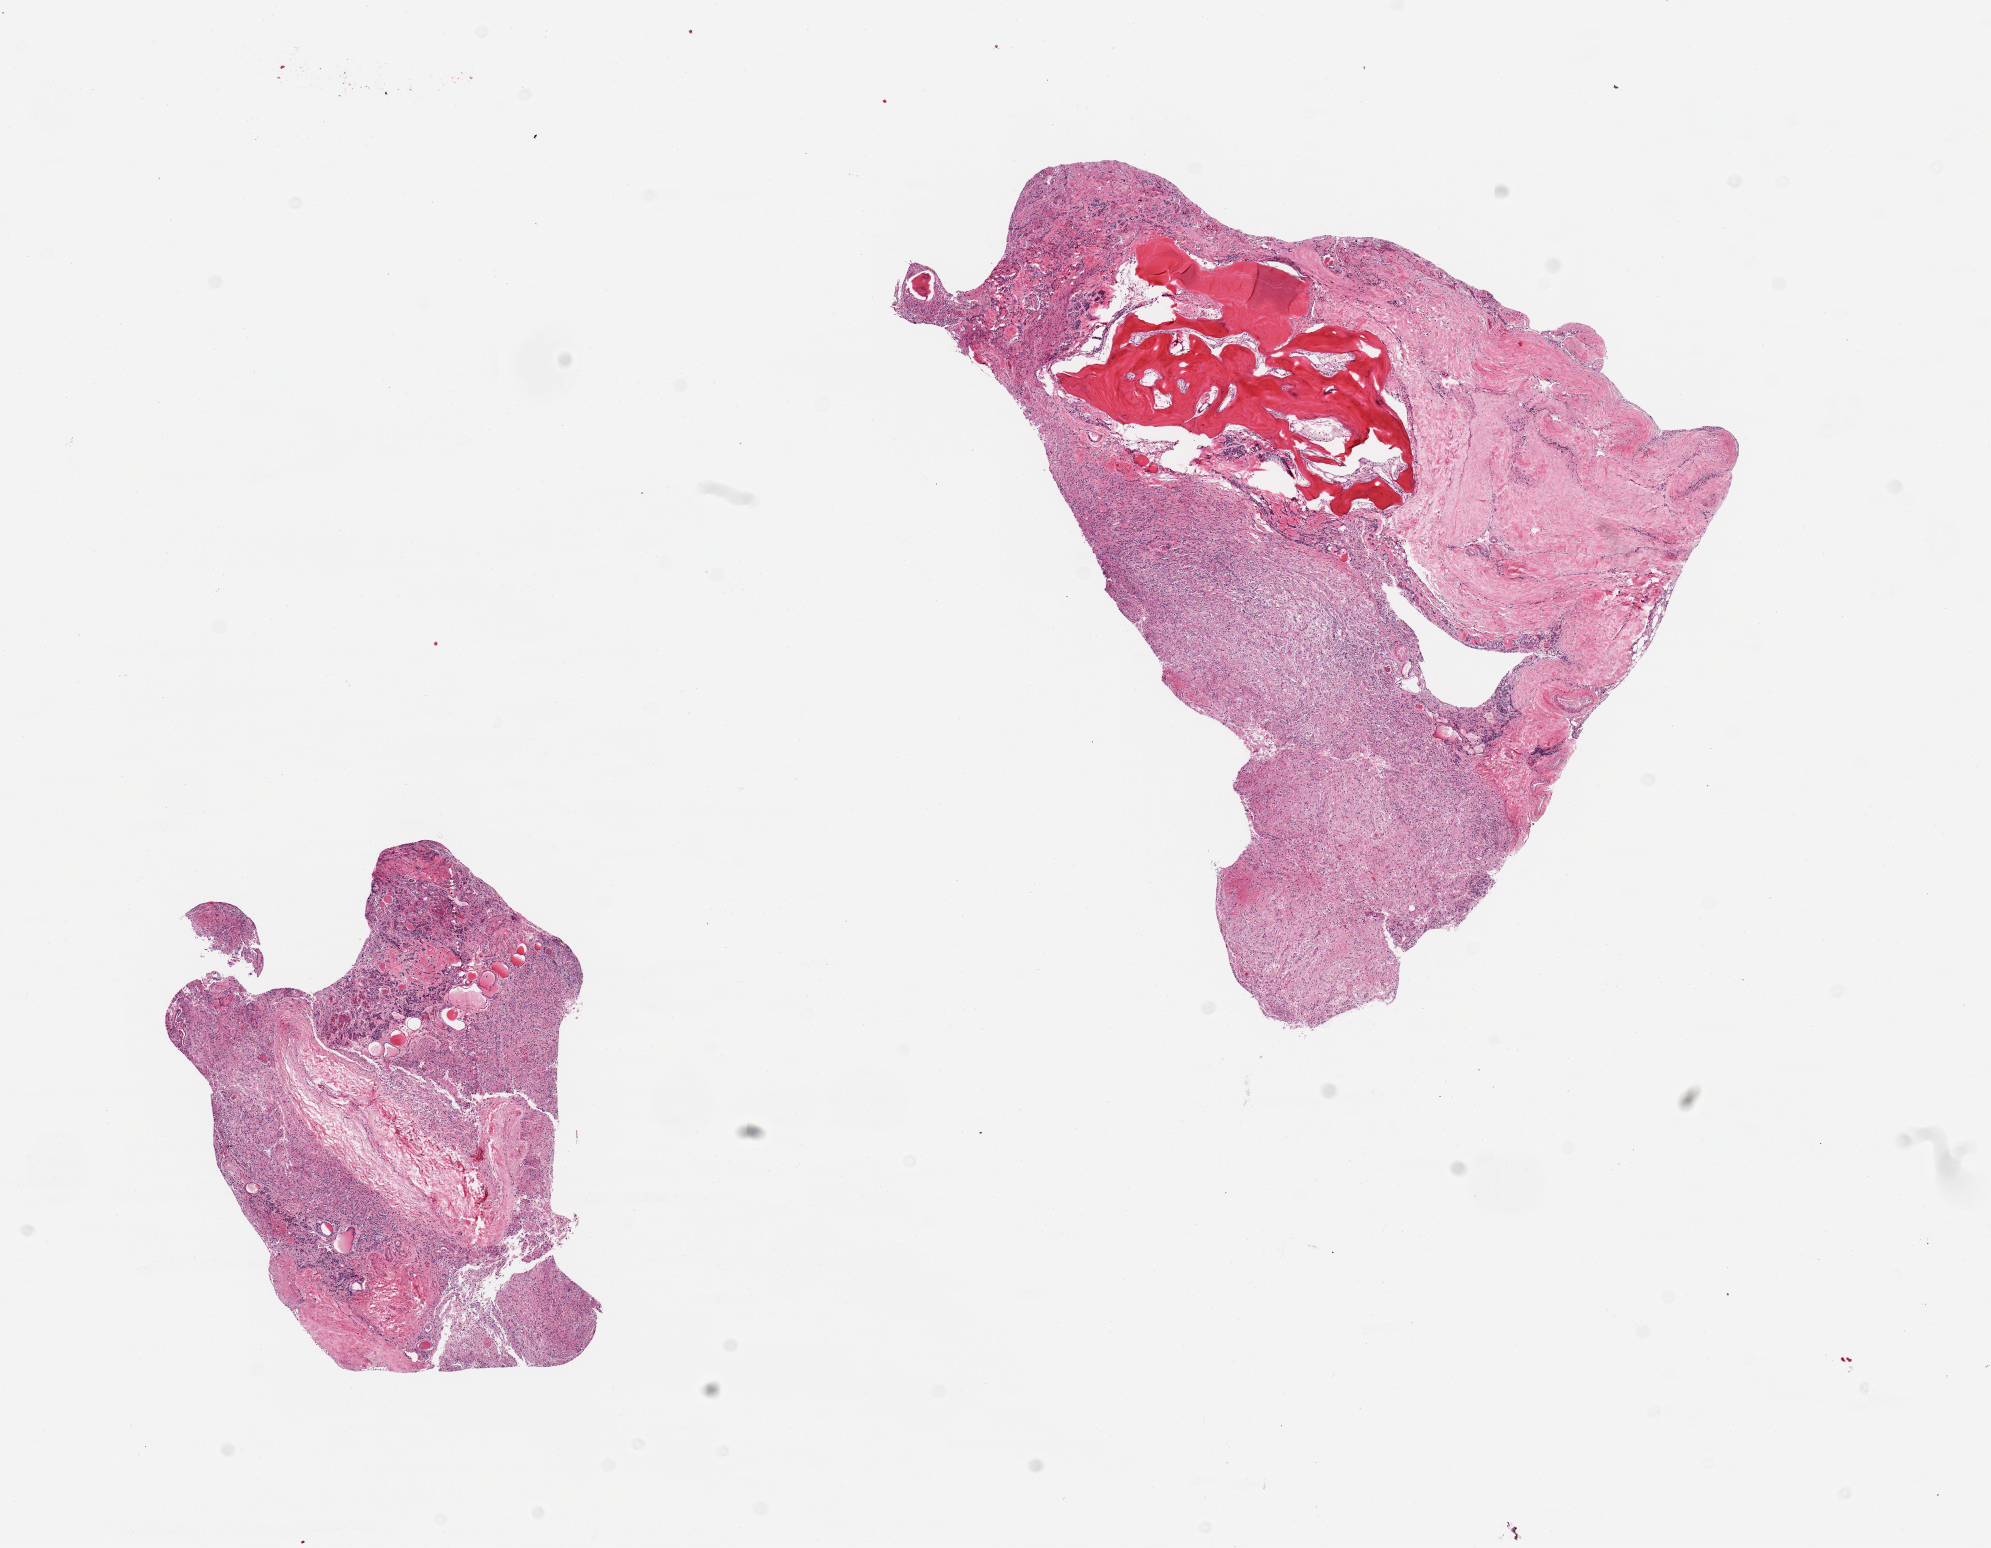
Whole-slide image, hematoxylin and eosin (H&E) stain, a low-resolution overview of the entire scanned area, about 15.8 x 12.2 mm (slide scanned at 20x). PAXgene-fixed paraffin-embedded (PFPE) section. Sampled site (target tissue): pituitary. Donor tissue sample. Donor: female.
* review note (as recorded): 2 pieces; mostly neurohypophysis; also pars intermedia, bone and dura